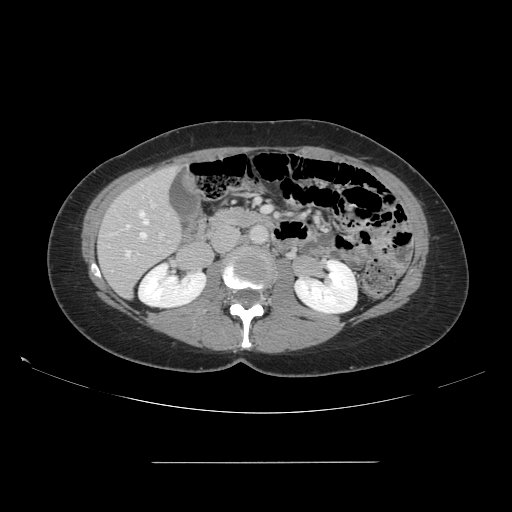
Contrast-enhanced abdominal CT, one axial slice. Position 61 of 151 along the scan axis. 120 kVp. Soft-tissue window (W 400 / L 40 HU). 2.5 mm slice thickness. 512 × 512 image matrix. Female patient, age 46 years. From the clinical record (not read from this slice): diagnosis: colorectal cancer liver metastases, imaged before liver resection; multiple liver metastases: yes; largest metastasis: 3 cm; disease in both lobes: yes.
Structures marked on this image (expert manual segmentation):
- hepatic veins: bounding box [x1, y1, x2, y2] px = [126, 210, 149, 257]
- liver: [99, 167, 181, 296]
- planned liver remnant (the part of the liver to remain after resection): [99, 167, 181, 297]
- portal vein (with intrahepatic branches): [150, 200, 163, 237]